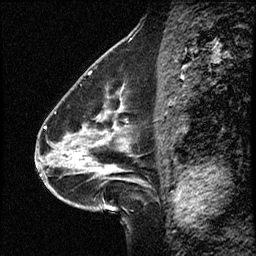
Breast MRI (dynamic contrast-enhanced), one sagittal slice. Position 26 of 50 along the scan axis. Dynamic contrast-enhanced study with each time point stored as its own series, time point 2 of 4 at this slice position (early post-contrast, ordered by acquisition time). 1.5 T. TE 4.2 ms, TR 17.5 ms. 3 mm slice thickness. 256 × 256 image matrix. Case-level facts recorded for this patient, not image findings: setting: breast cancer imaged before/during neoadjuvant chemotherapy.
Outlined on this slice (semi-automatically segmented with operator editing):
- analysis volume of interest (the breast-tissue region the enhancement analysis was run in; not a lesion): bounding box [x1, y1, x2, y2] px = [52, 98, 158, 207]
- tumour enhancement mask (voxels above the 100 % enhancement threshold inside the analysis volume of interest): [75, 154, 109, 172]